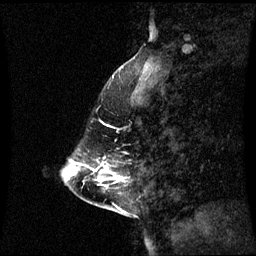
Breast MRI (dynamic contrast-enhanced), one sagittal slice. Position 18 of 60 along the scan axis. Dynamic contrast-enhanced series, image 2 of 3 at this slice position (ordered by acquisition). 1.5 T. TE 4.2 ms, TR 8.9 ms. 2.3 mm slice thickness. 256 × 256 image matrix. Female patient, age 43 years. From the clinical record (not read from this slice): setting: breast cancer imaged before/during neoadjuvant chemotherapy; receptor status: HR-positive, HER2-negative.
Structures marked on this image (semi-automatically segmented with operator editing):
- analysis volume of interest (the breast-tissue region the enhancement analysis was run in; not a lesion): box from (x=78, y=162) to (x=126, y=189) px
- tumour enhancement mask (voxels above the 70 % enhancement threshold inside the analysis volume of interest): (x=101, y=170)–(x=103, y=173)